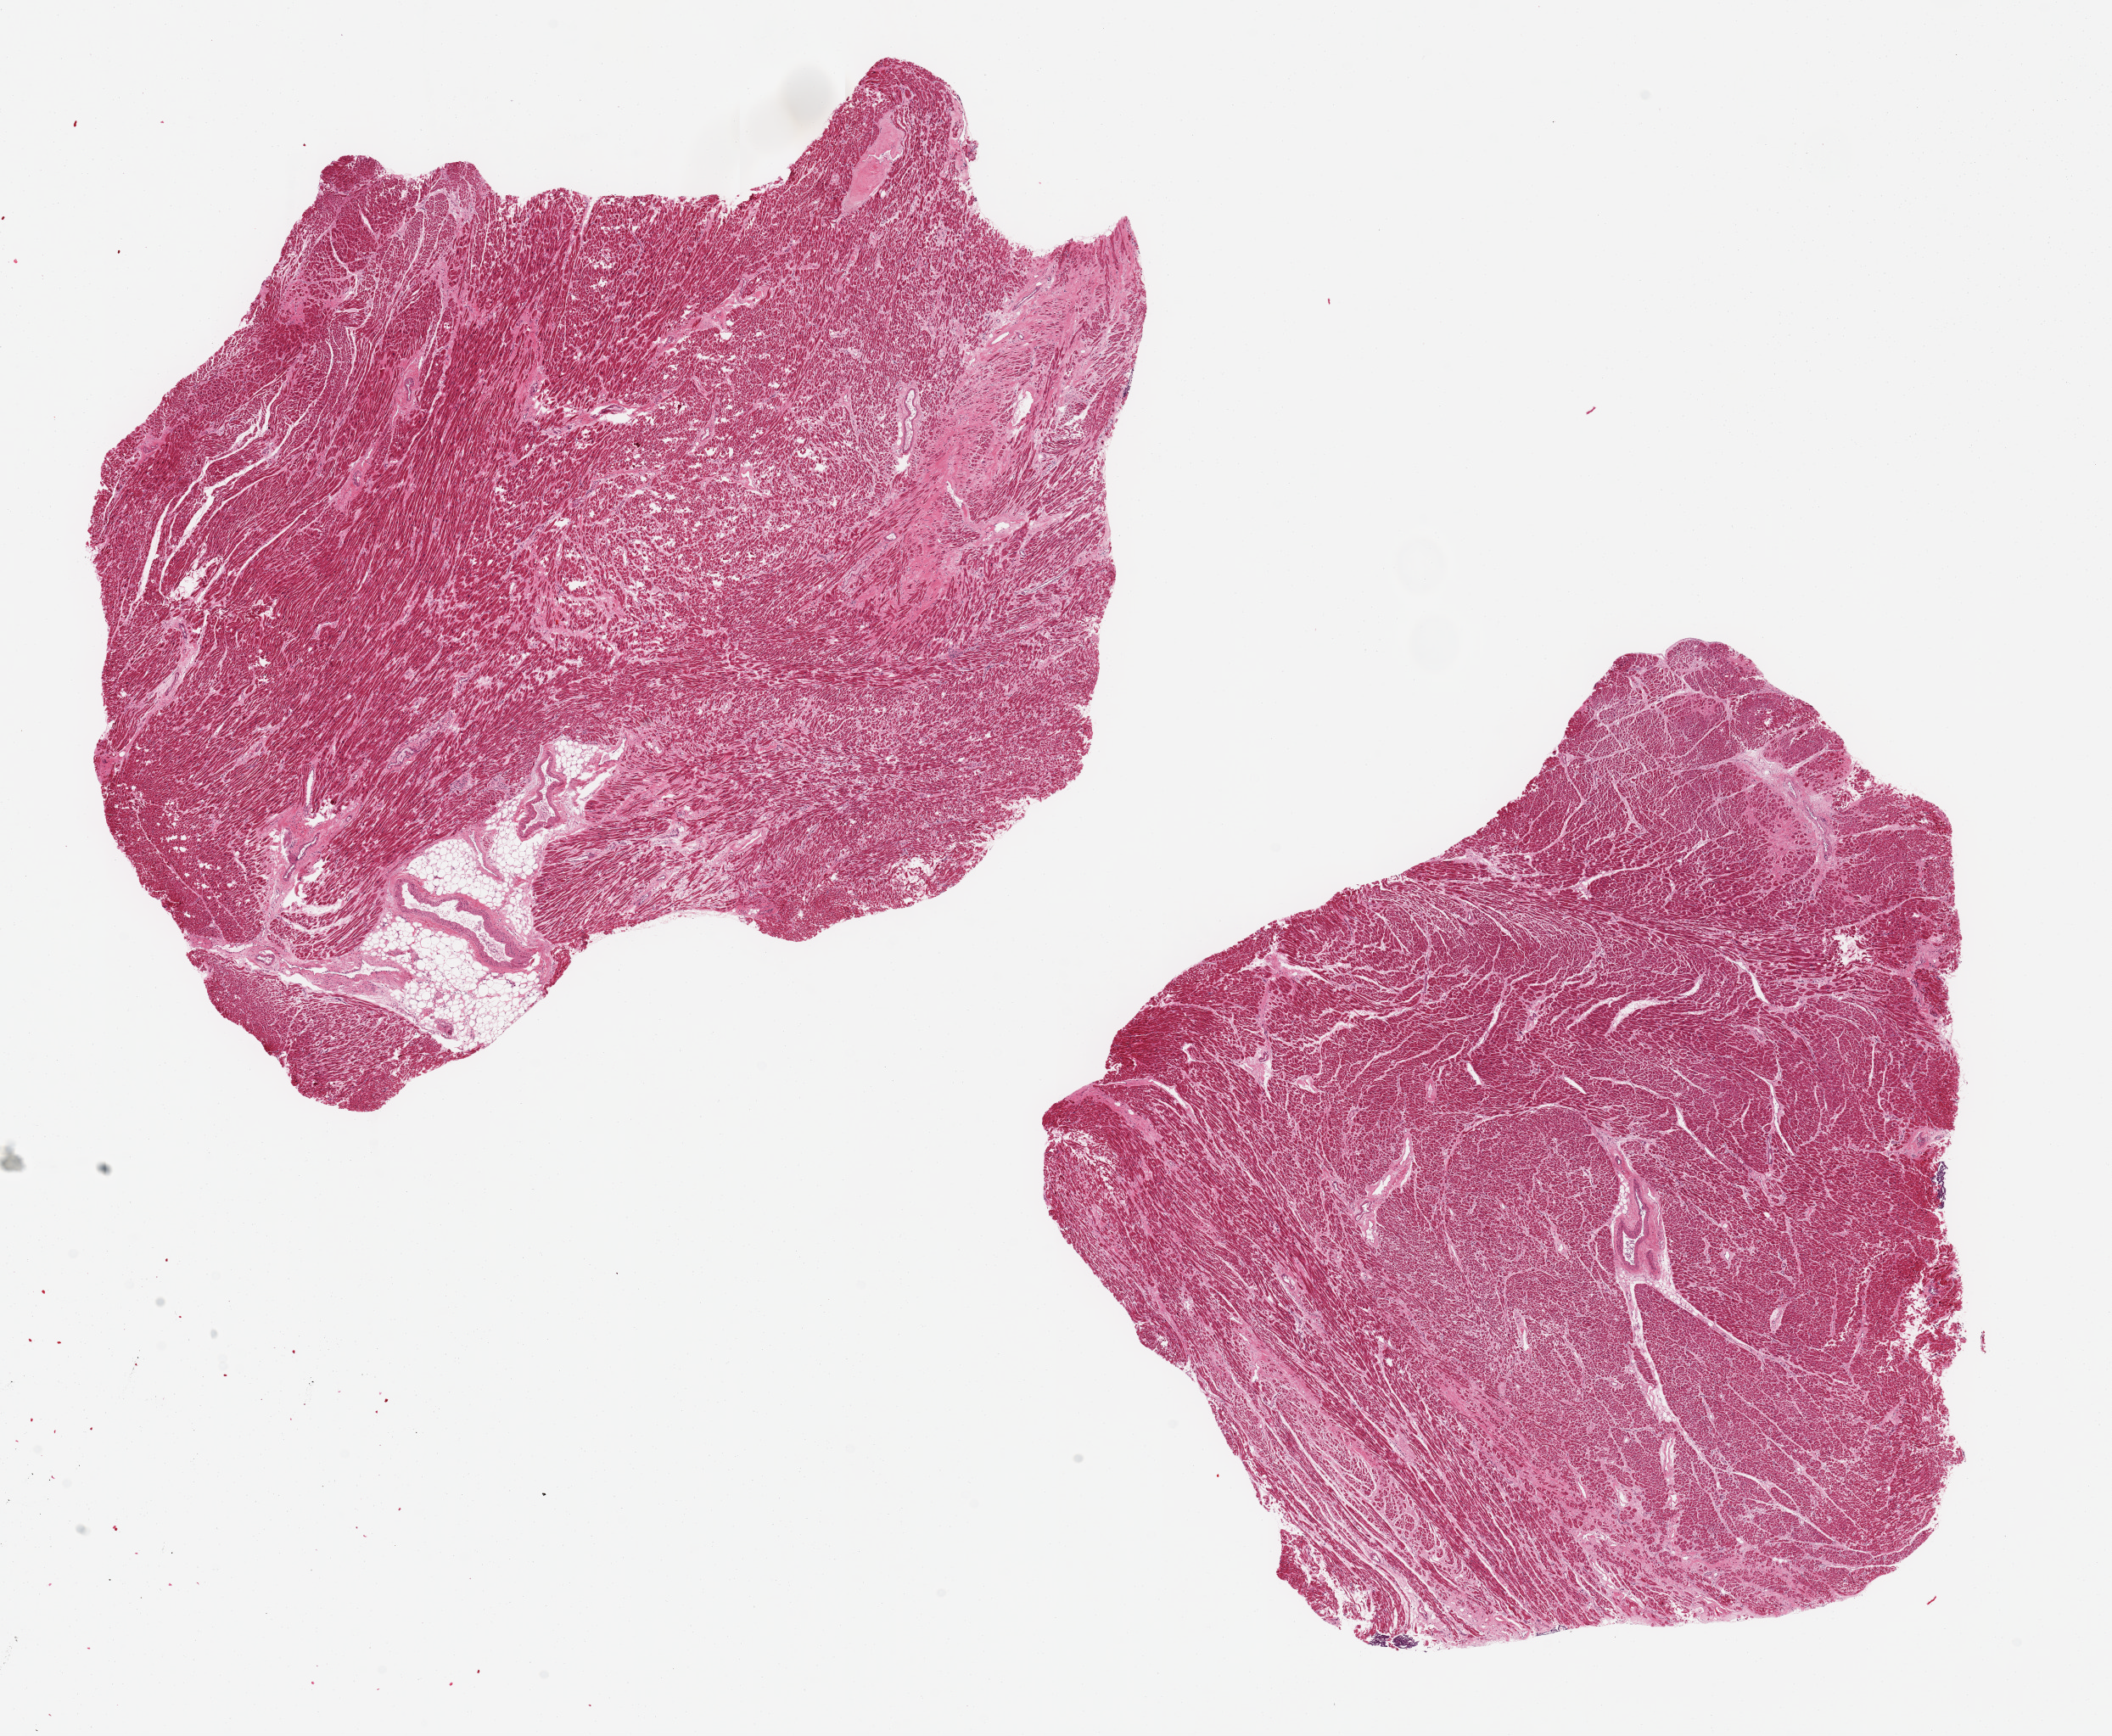
Digitized H&E-stained section — shown as a low-resolution overview of the whole scanned area (about 19.7 x 16.2 mm); PAXgene-fixed, paraffin-embedded tissue; section of heart (target tissue); tissue donor sample. Male donor.
Pathologist's review note for this sample: 2 ~ 9.5x7.5mm pieces. Patchy fibrosis consistent with remote infarcts present in both.